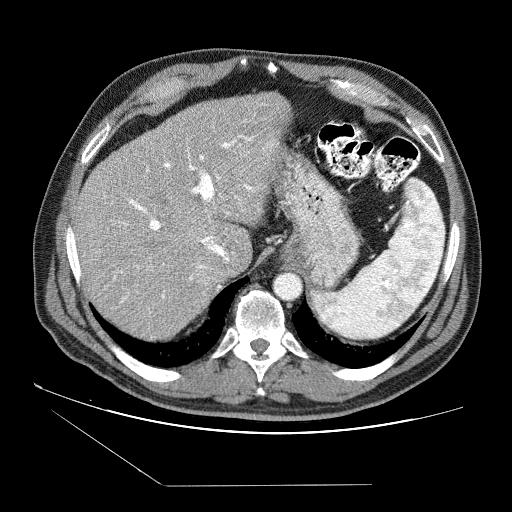
Contrast-enhanced abdominal CT (liver protocol), one axial slice; position 60 of 87 along the scan axis; reconstruction kernel STANDARD; soft-tissue window (W 400 / L 40 HU); 2.5 mm slice thickness; 512 × 512 image matrix, field of view 400 × 400 mm. Case-level facts recorded for this patient, not image findings: diagnosis: hepatocellular carcinoma (patient treated with transarterial chemoembolisation; whether this scan precedes or follows treatment is not stated here); TNM stage (as recorded): Stage-II; Child-Pugh class: B; tumour differentiation: no biopsy; tumour nodularity: multinodular.
Structures marked on this image (semi-automatic segmentation, software-assisted and operator-edited):
- liver parenchyma outside the tumour (the mass and vessels are separate outlines, so this box may not span the whole liver): box from (x=75, y=92) to (x=292, y=338) px
- mass: (x=196, y=269)–(x=214, y=285)
- liver vessels: (x=113, y=135)–(x=273, y=313)